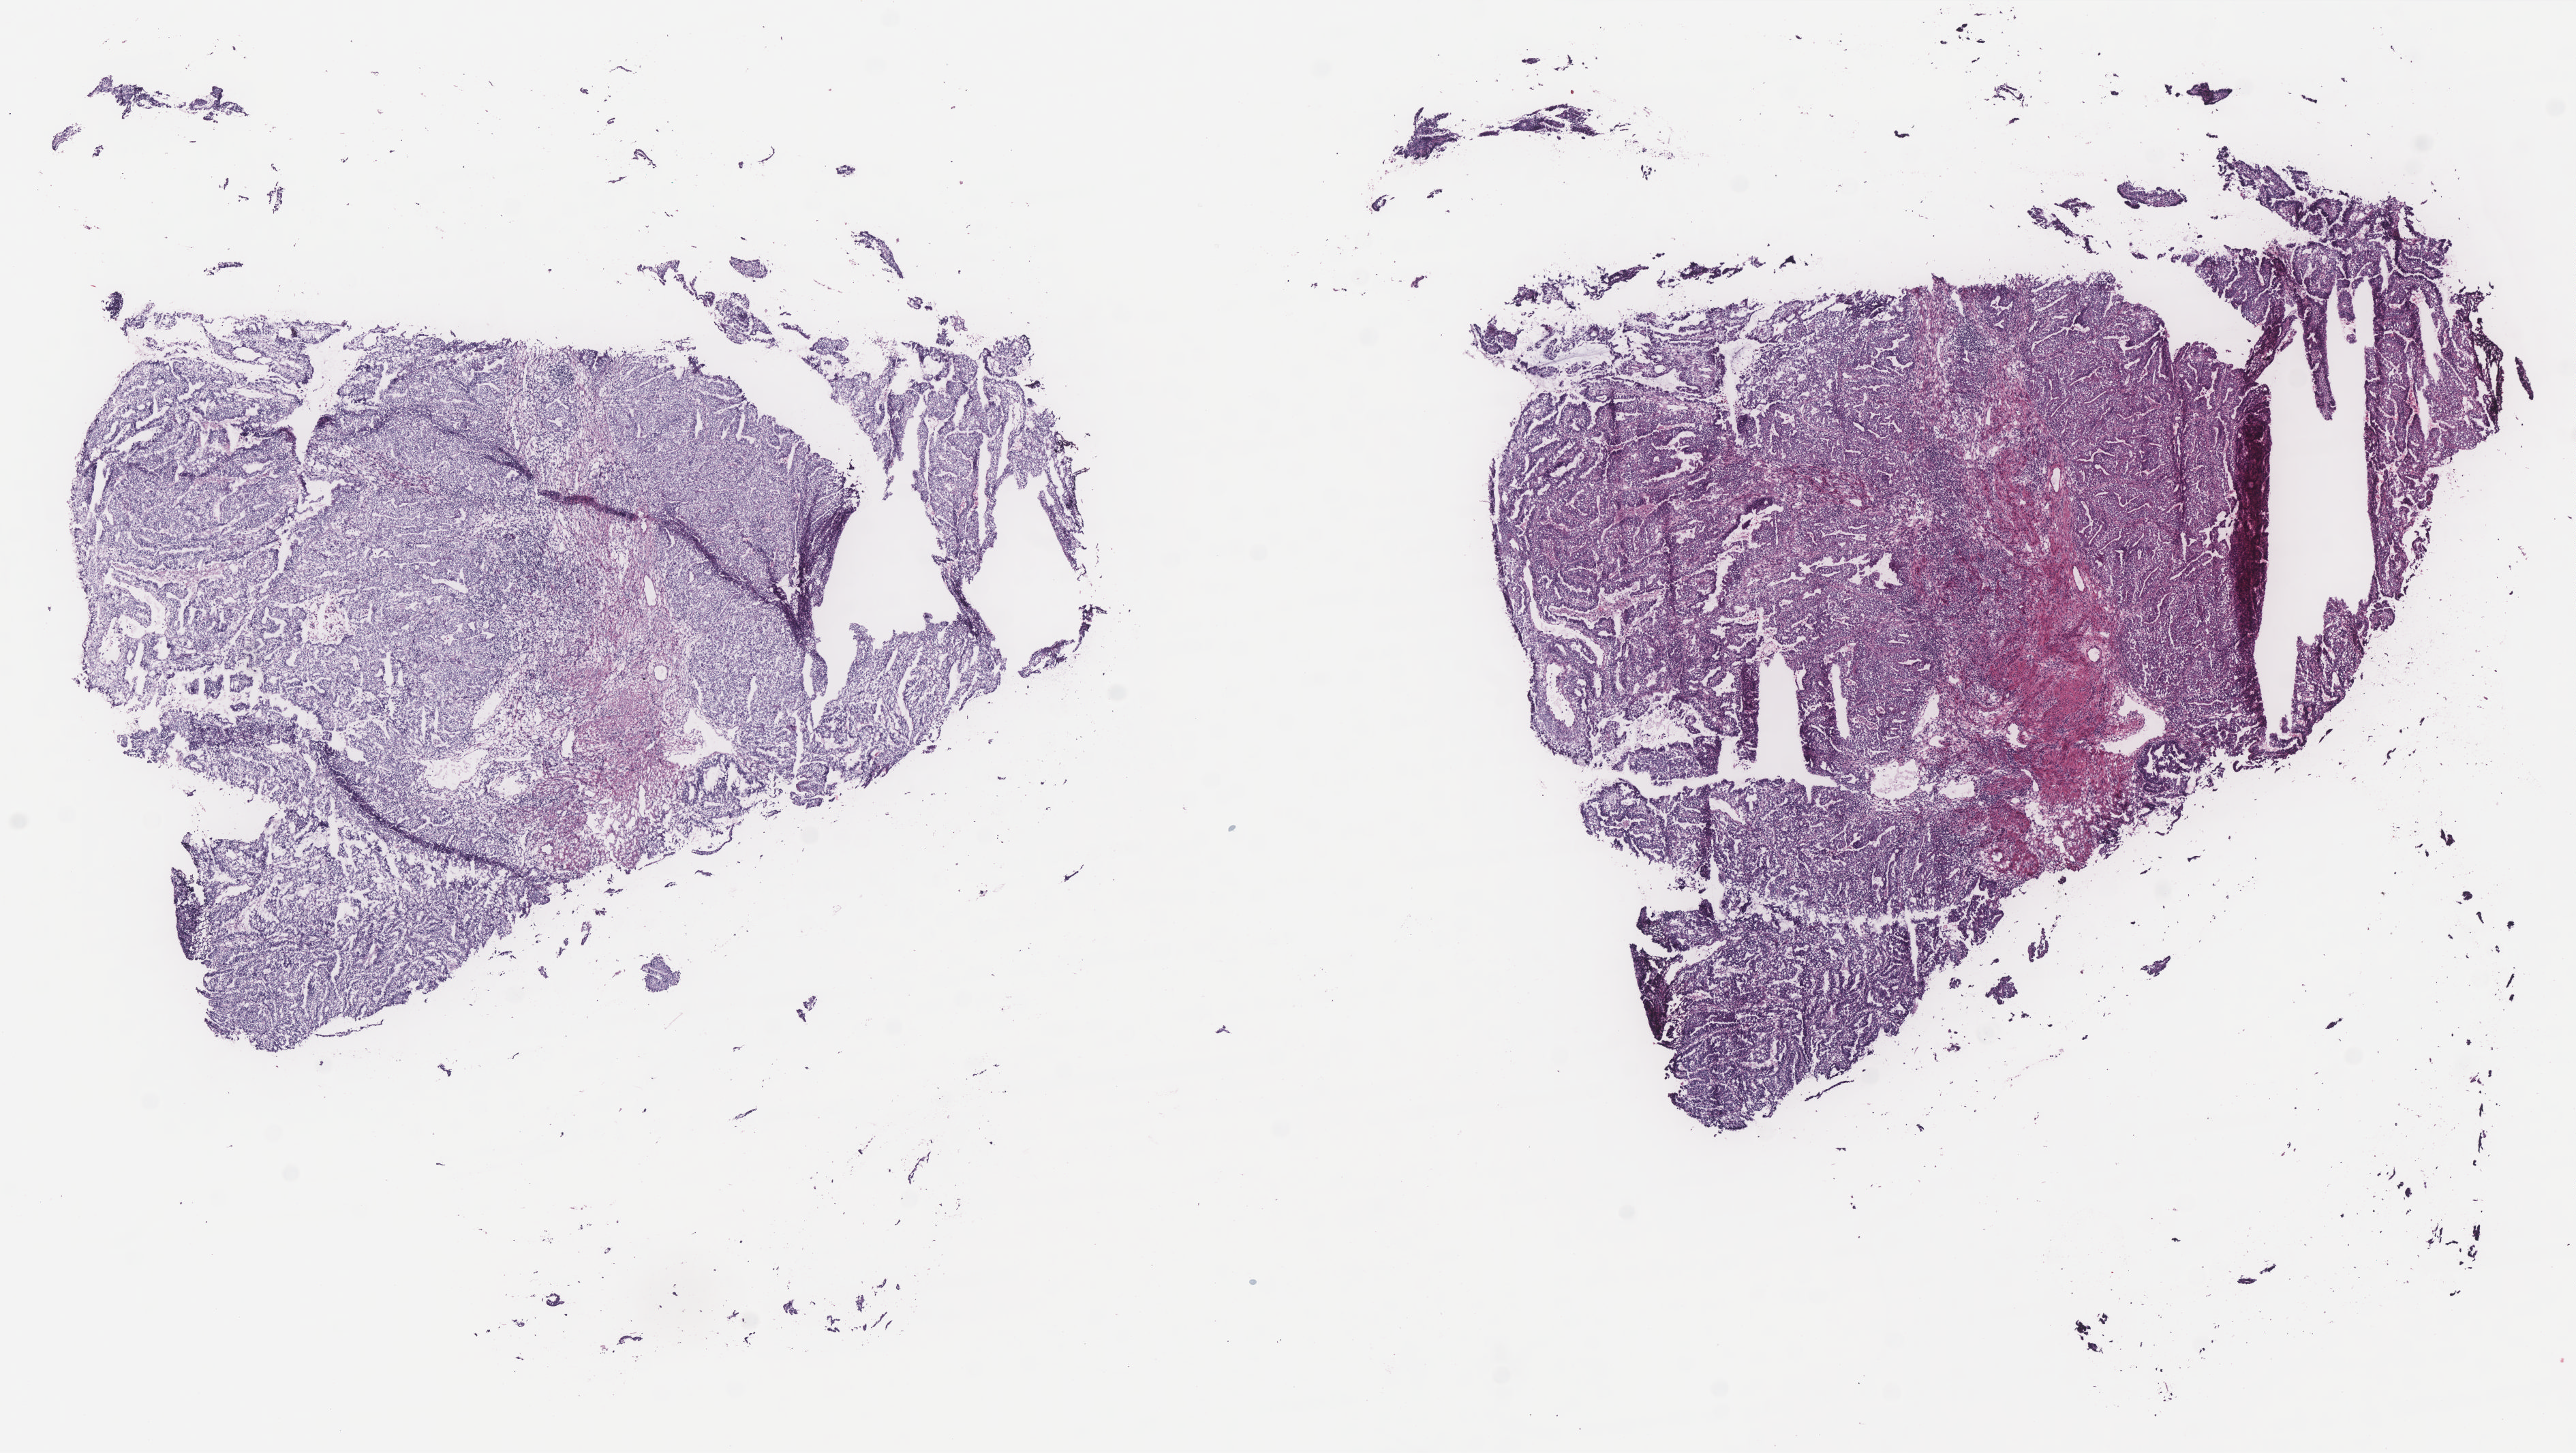
Digitized H&E-stained tissue section (whole slide) — a low-resolution overview of the entire scanned area, about 15.2 x 8.5 mm (slide scanned at 40x); frozen section from the bottom of the tissue portion; sample: primary tumour, uterus. Patient: female, age at initial diagnosis 63 years. Histologic grade: G2 (moderately differentiated). Composition of this section per pathologist review: tumour cells 80%, tumour nuclei 80%, normal cells 0%, stromal cells 15%, necrosis 5%. Infiltration values recorded for this section: lymphocyte infiltration 30%, monocyte infiltration 10%, neutrophil infiltration 40%.
FIGO stage: IC. Diagnosis: Endometrioid adenocarcinoma, NOS (endometrium).